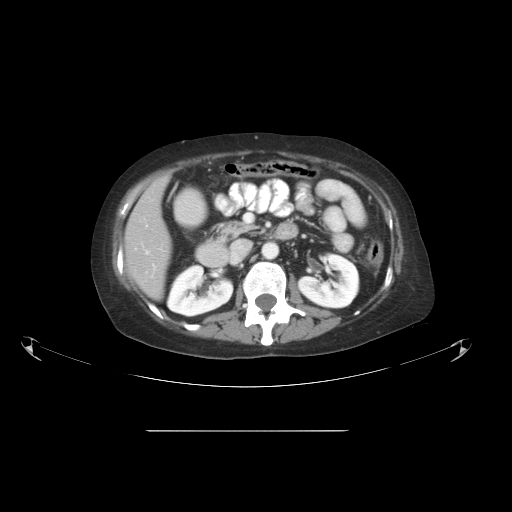
Contrast-enhanced abdominal CT, one axial slice. Position 25 of 51 along the scan axis. Reconstruction kernel STANDARD. 120 kVp. Intravenous contrast given. Soft-tissue window (W 400 / L 40 HU). 5 mm slice thickness. 512 × 512 image matrix, field of view 475 × 475 mm. Female patient, age 48 years. Case-level facts recorded for this patient, not image findings: diagnosis: colorectal cancer liver metastases, imaged before liver resection; multiple liver metastases: yes; largest metastasis: 1 cm; disease in both lobes: no.
Structures marked on this image (expert manual segmentation):
- hepatic veins: bounding box [x1, y1, x2, y2] px = [145, 251, 149, 254]
- liver: [126, 178, 172, 299]
- planned liver remnant (the part of the liver to remain after resection): [126, 178, 172, 300]